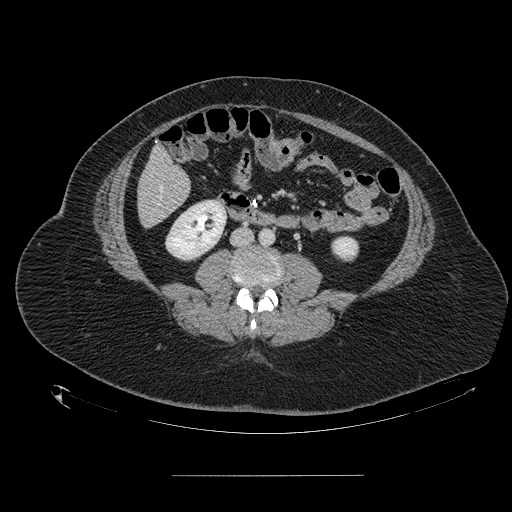
Contrast-enhanced abdominal CT, one axial slice. Slice 31 of 164 in the series (ordered by position). 120 kVp. Intravenous contrast given. Soft-tissue window (W 400 / L 40 HU). 2.5 mm slice thickness. 512 × 512 image matrix, field of view 495 × 495 mm. Female patient, age 52 years. From the clinical record (not read from this slice): diagnosis: colorectal cancer liver metastases, imaged before liver resection; multiple liver metastases: yes; largest metastasis: 3.5 cm; disease in both lobes: no.
Structures marked on this image (outlined manually by an expert reader):
- hepatic veins: bounding box <160,186,162,188> (left, top, right, bottom; pixels)
- liver: <139,149,190,227>